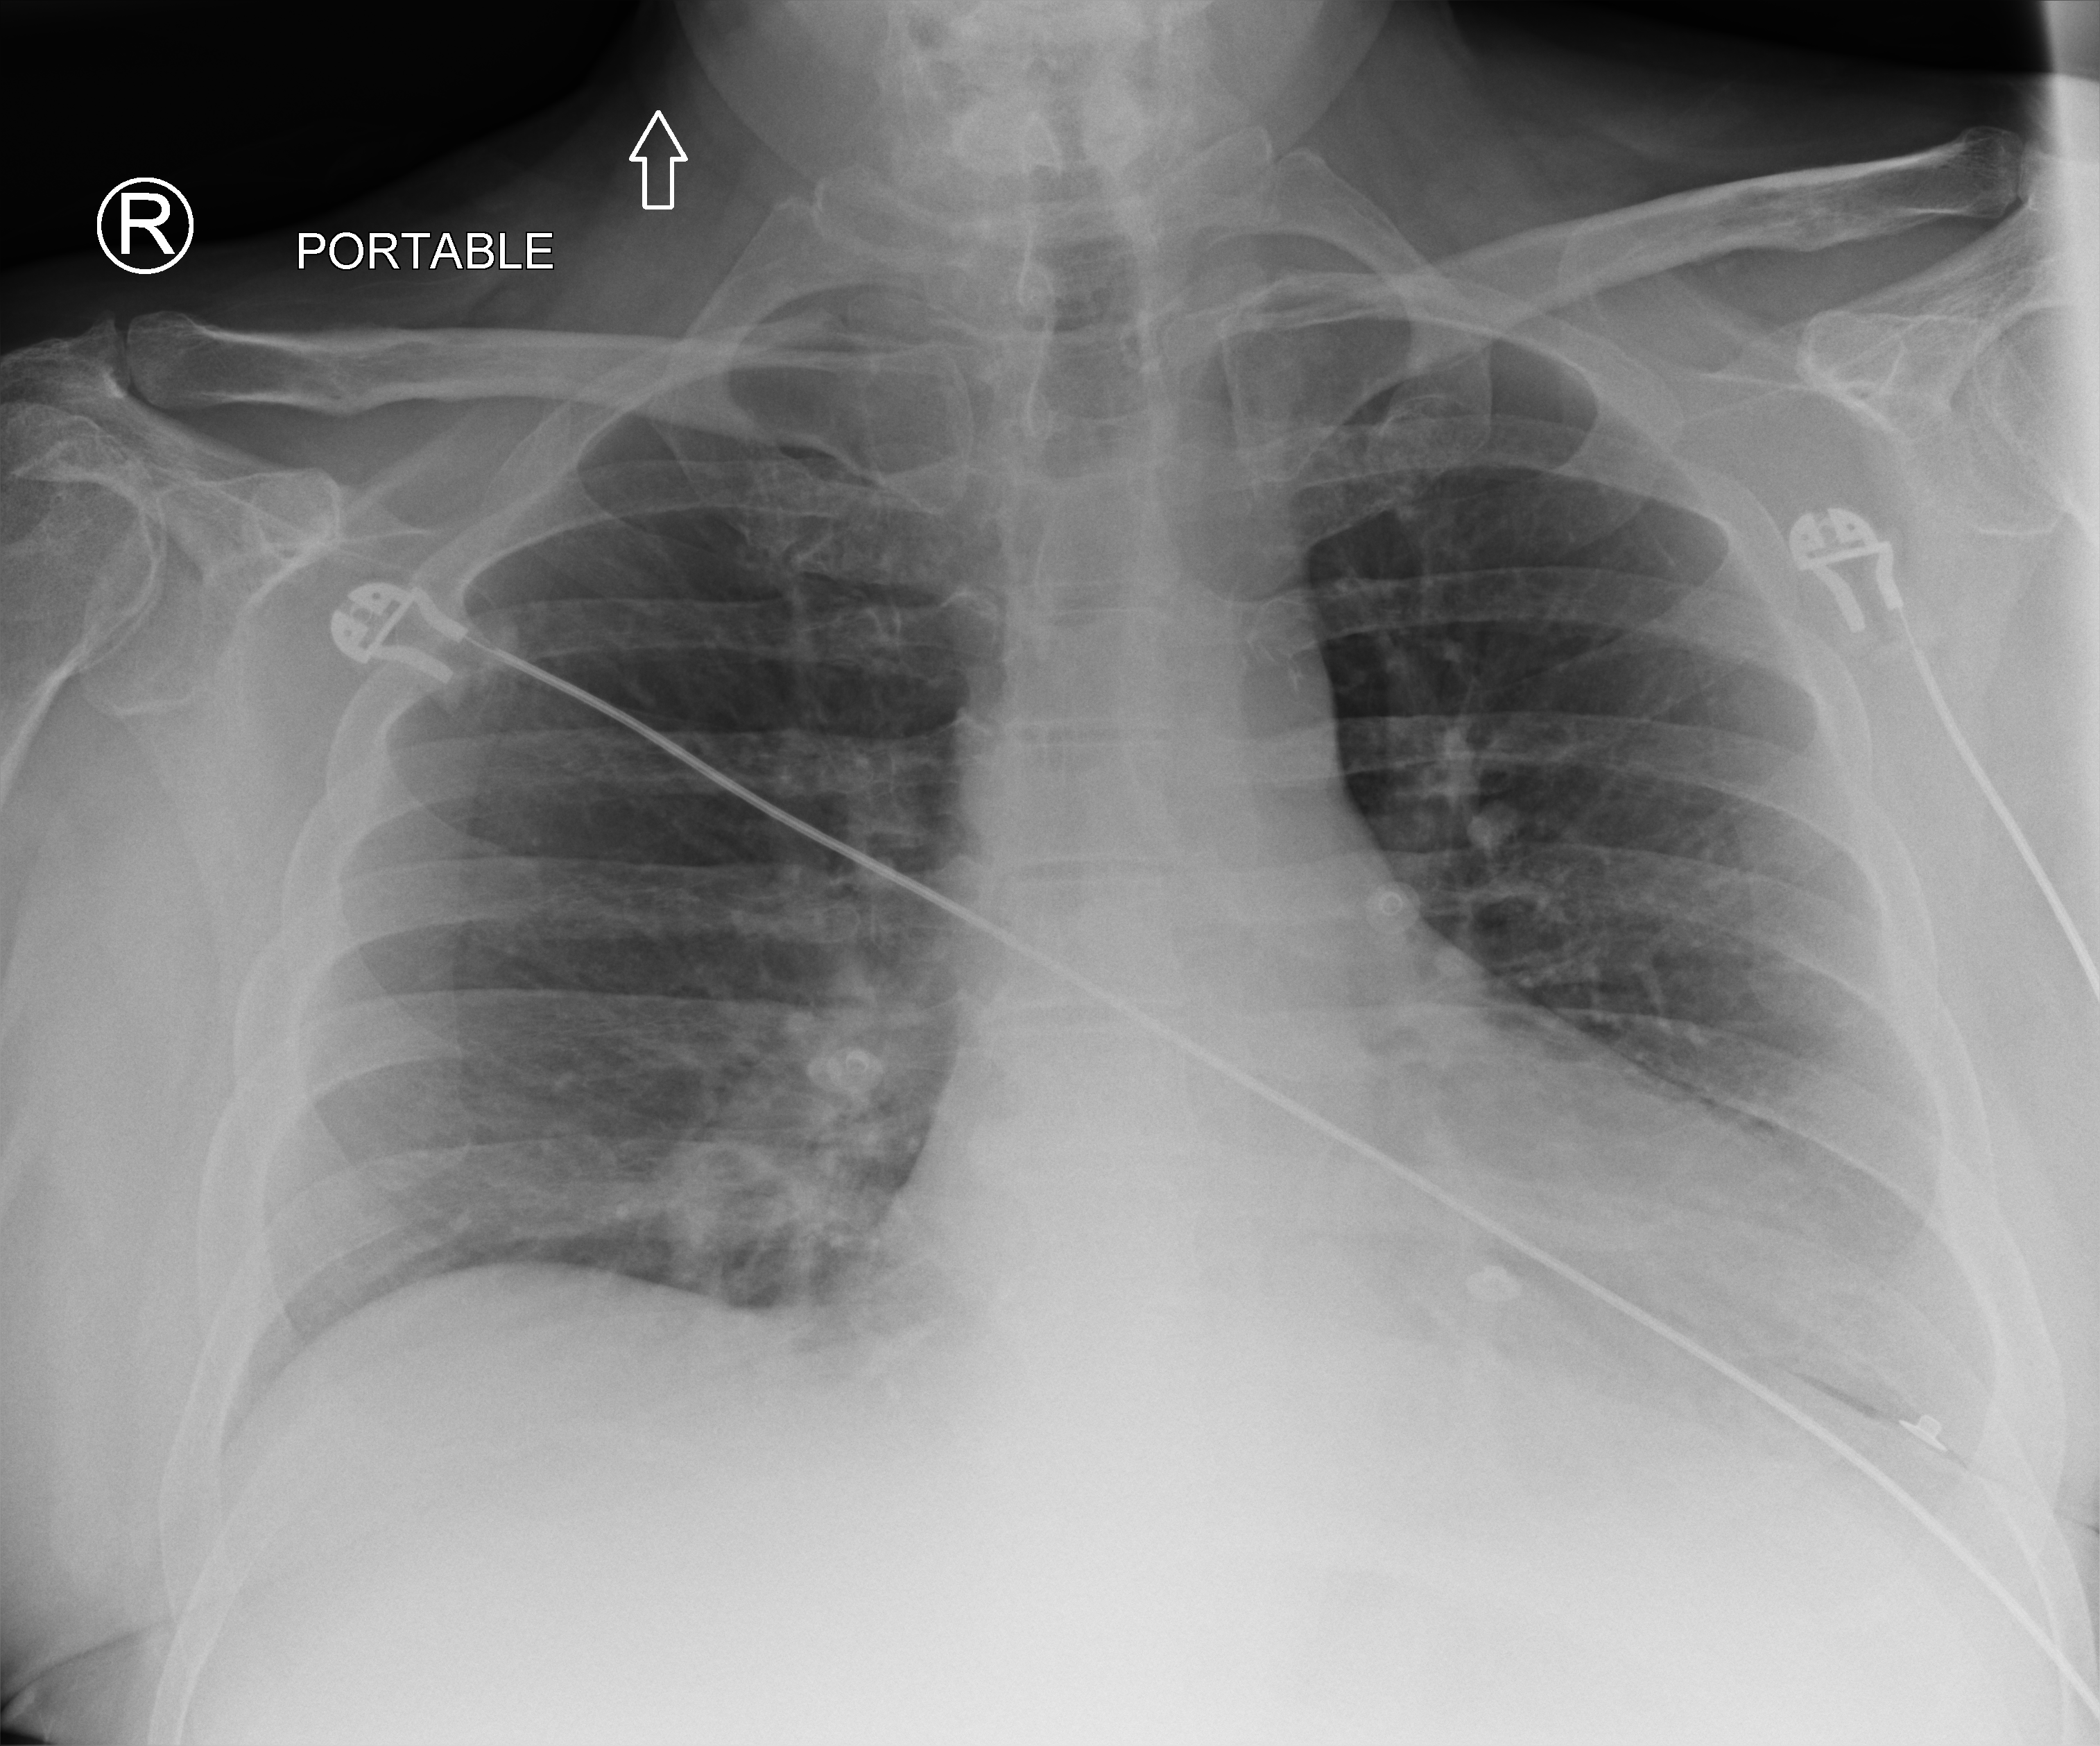
Portable chest radiograph; anteroposterior (AP) projection. Patient hospitalised with COVID-19; male, aged 60–74 years.
From the hospital-stay record, not from the radiograph (when in the stay this image was taken is not recorded):
- mechanically ventilated during this hospital stay: no
- admitted to intensive care during this hospital stay: no